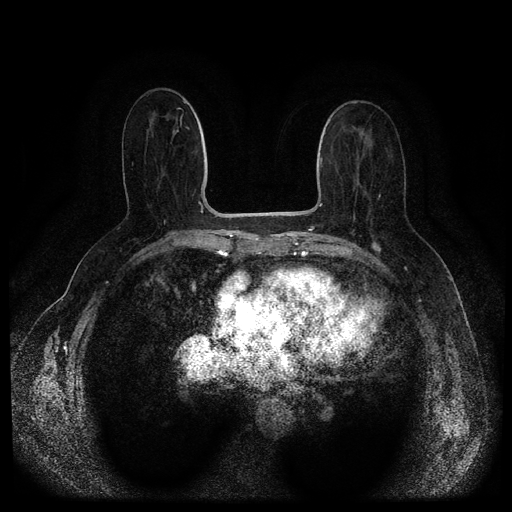
Breast MRI (dynamic contrast-enhanced, multi-phase), one axial slice. Position 47 of 116 along the scan axis. Dynamic contrast-enhanced series, time point 2 of 5 at this slice position (early post-contrast). 1.5 T. TE 2.6 ms, TR 5.4 ms. 2 mm slice thickness. 512 × 512 image matrix, field of view 340 × 340 mm. Female patient, age 67 years.
Outlined on this slice (semi-automatic segmentation, software-assisted and operator-edited):
- breast lesion (labelled 'tumour' in the annotation; benign lesions carry a separate 'benign' label): box from (x=370, y=242) to (x=383, y=253) px